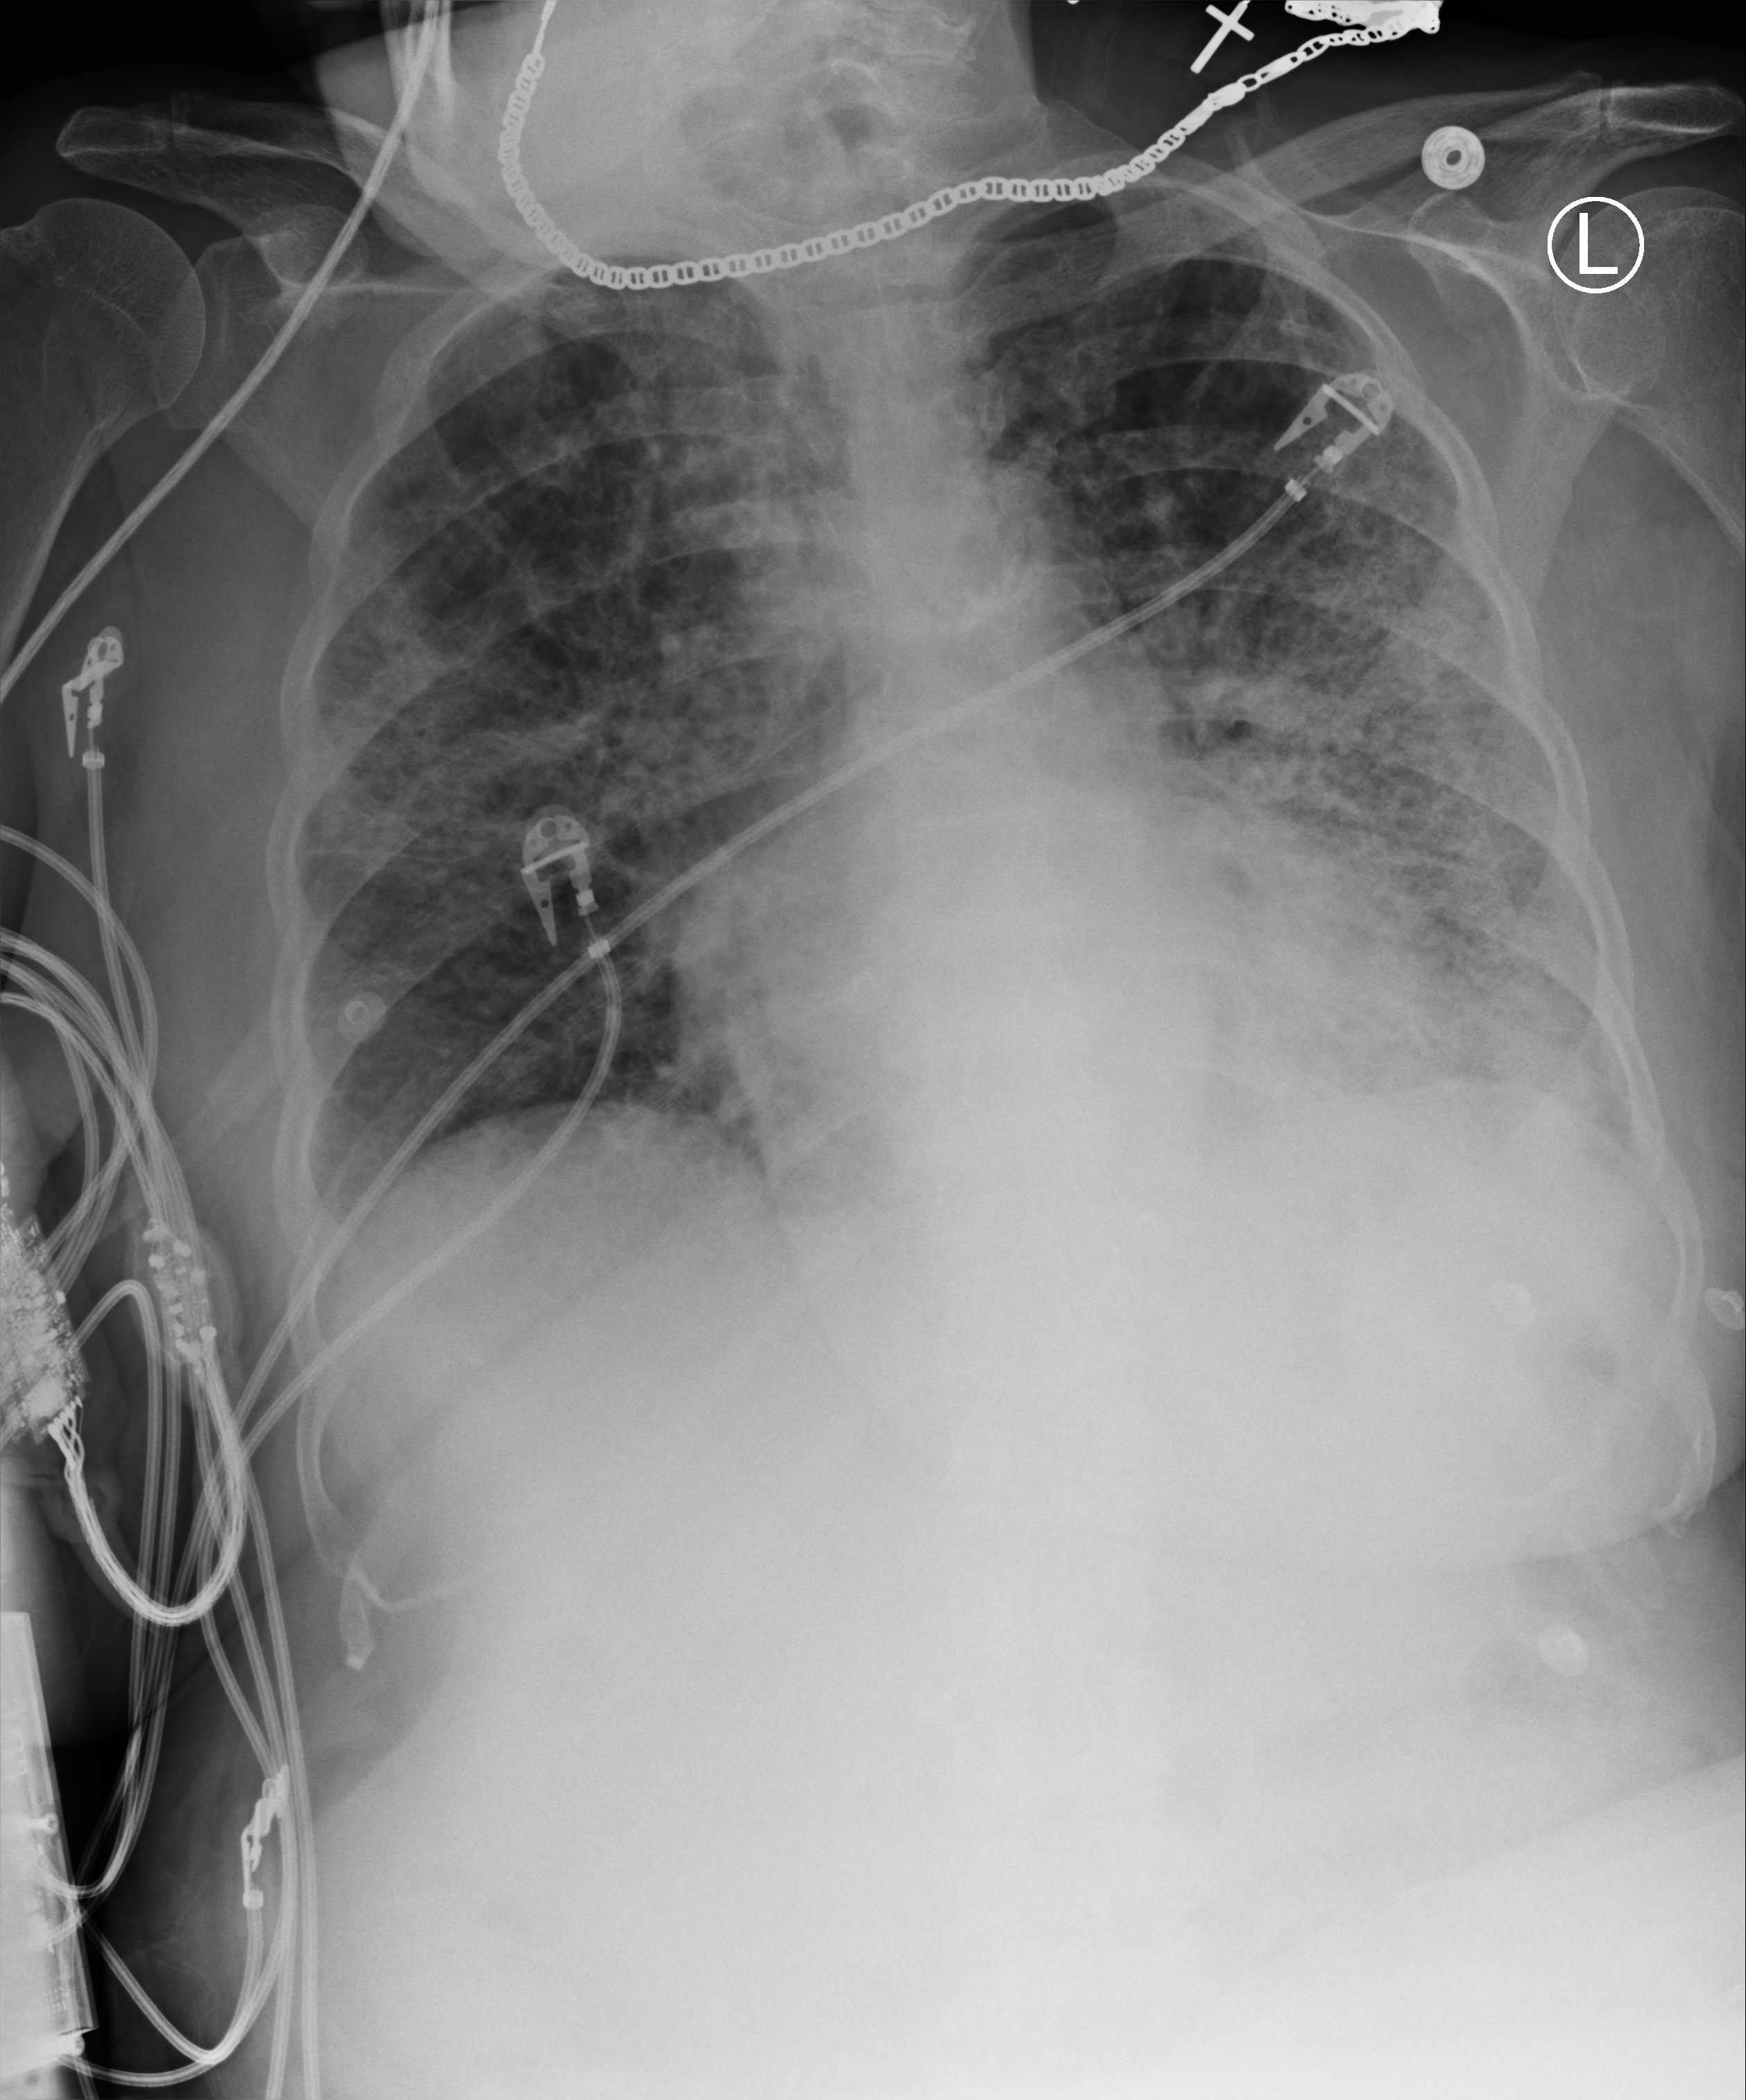
Chest X-ray (portable), anteroposterior (AP) projection. Patient hospitalised with COVID-19; female, aged 75–90 years.
Admission-level facts for this patient (not findings on this image; timing relative to this image not recorded): mechanically ventilated during this hospital stay: no; other chronic lung disease (admission record): no; admitted to intensive care during this hospital stay: no.